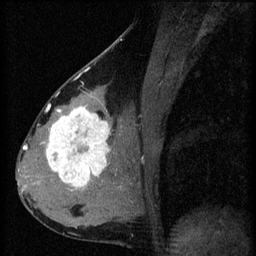
Breast MRI (dynamic contrast-enhanced), one sagittal slice; slice 30 of 60 in the series (ordered by position); 3 images stored at this slice position (order not interpretable as contrast timing); 1.5 T; TE 4.2 ms, TR 8.2 ms; 256 × 256 image matrix, field of view 180 × 180 mm. Patient: female, 37 years.
Outlined on this slice (semi-automatically segmented with operator editing):
- analysis volume of interest (the breast-tissue region the enhancement analysis was run in; not a lesion): box from (x=44, y=100) to (x=119, y=197) px
- tumour enhancement mask (voxels above the 70 % enhancement threshold inside the analysis volume of interest): (x=47, y=108)–(x=112, y=189)